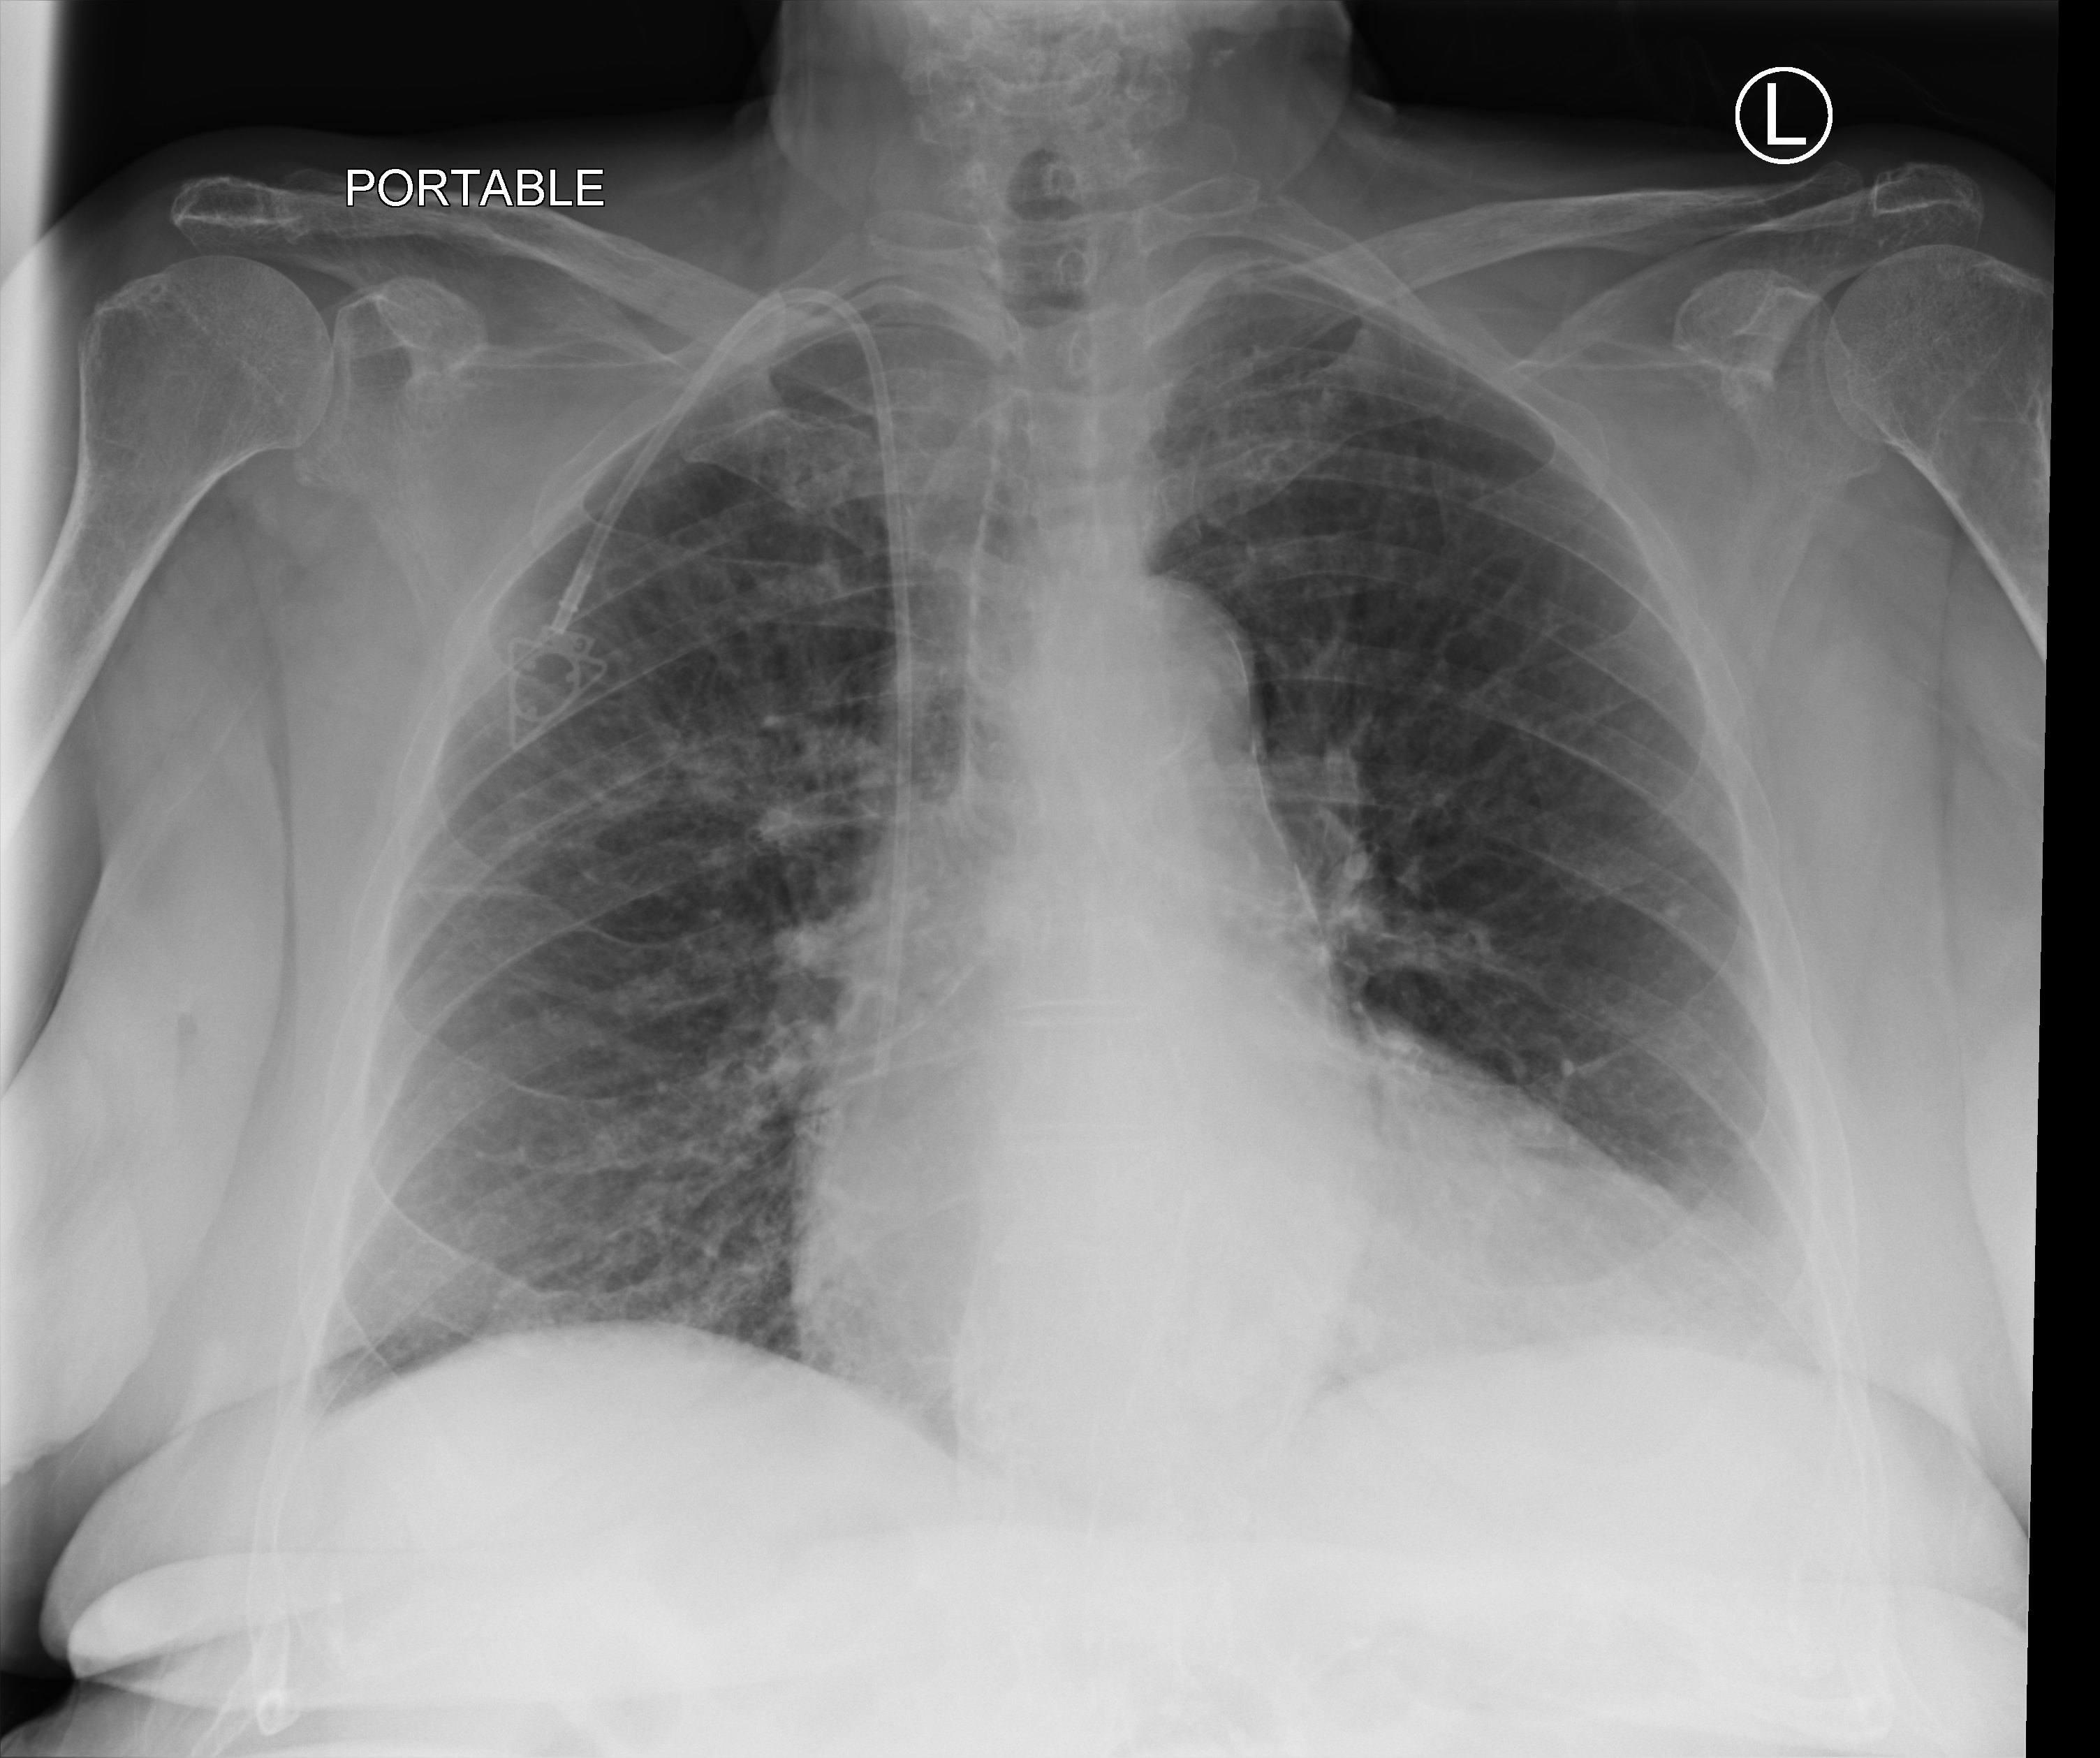
Chest X-ray (portable); anteroposterior (AP) projection. Female patient hospitalised with COVID-19, age 75–90 years.
From the hospital-stay record, not from the radiograph (when in the stay this image was taken is not recorded): admitted to intensive care during this hospital stay: no; mechanically ventilated during this hospital stay: no; length of hospital stay: 16 days.